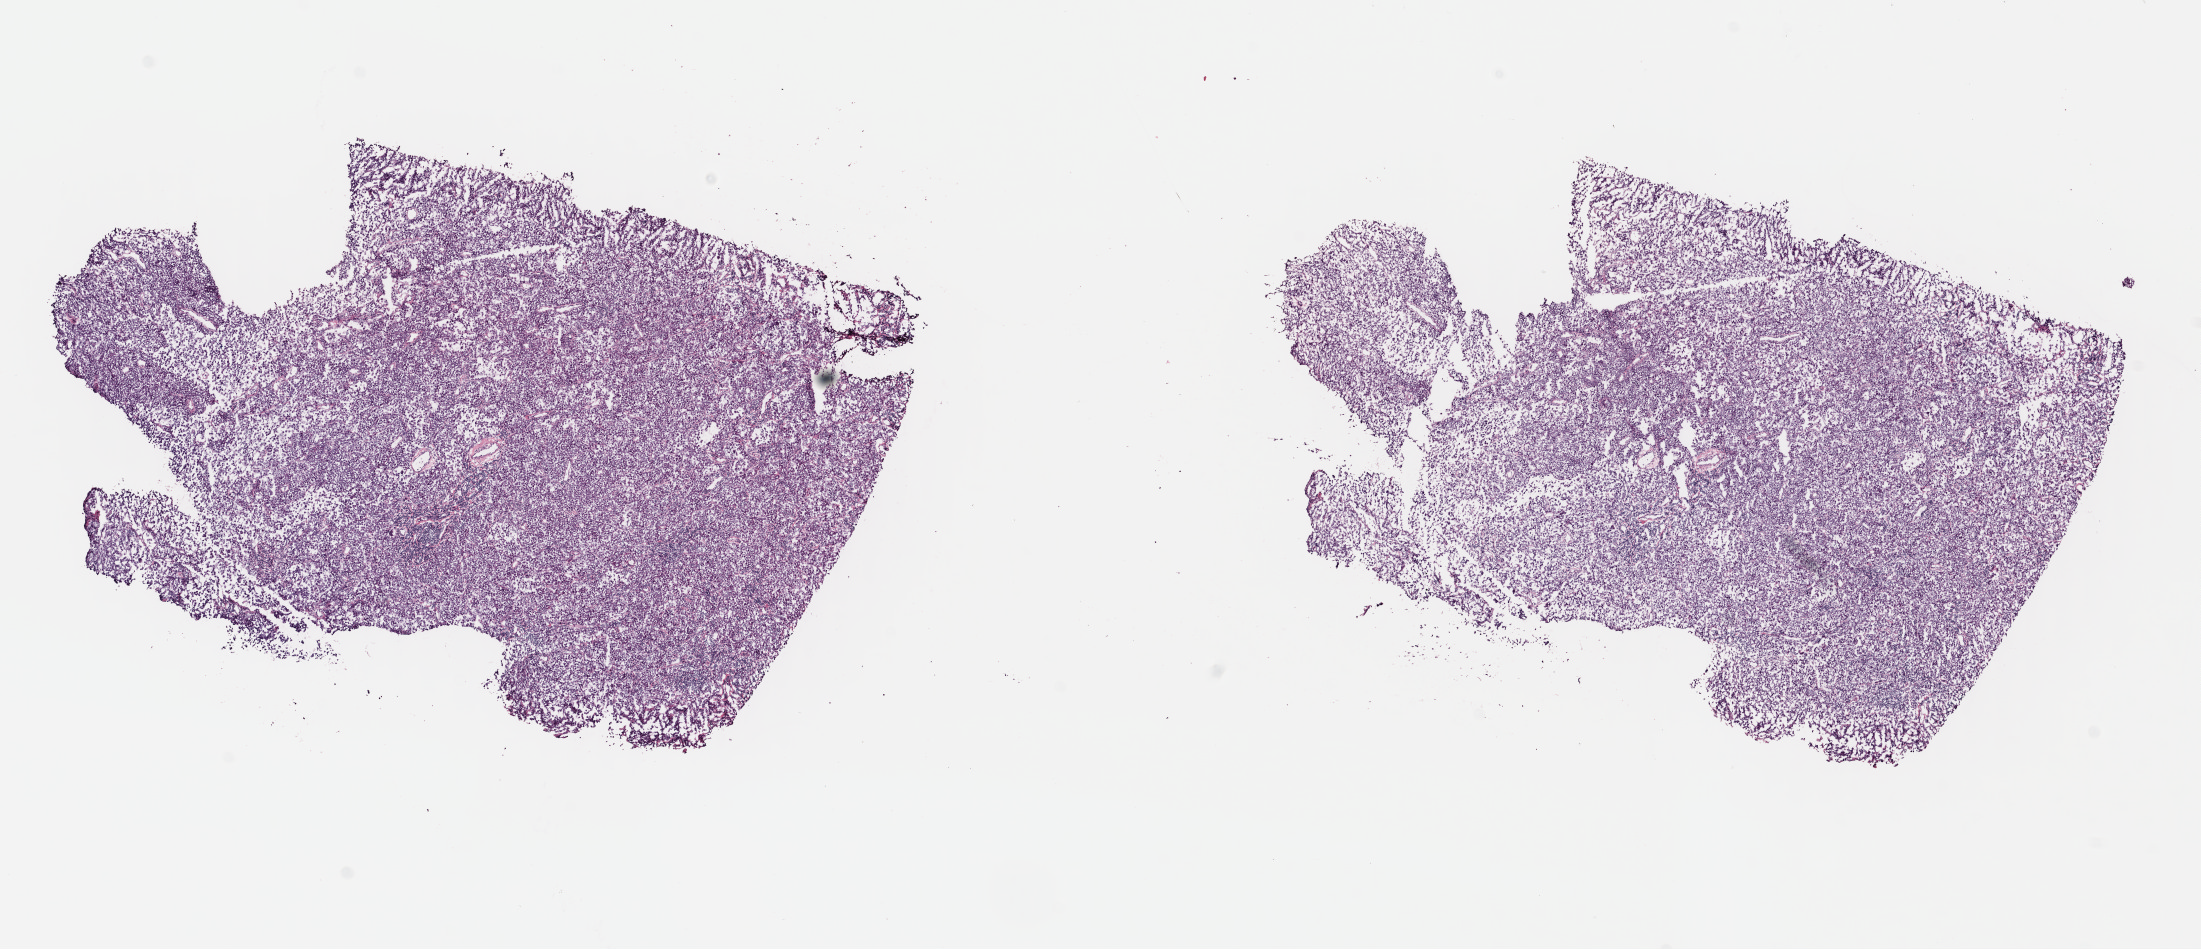
Digitized H&E tissue section (whole slide) — whole scanned area (about 17.3 x 7.5 mm, acquisition: 40x scan) shown as a low-resolution overview, frozen section, metastatic tumour sample. Patient: male, age at initial diagnosis 35 years. Slide review estimates, as recorded: tumour cells 80%, tumour nuclei 80%, normal cells 0%, stromal cells 20%, necrosis 0%. Infiltration values recorded for this section: lymphocyte infiltration 3%, monocyte infiltration 1%, neutrophil infiltration 0%.
• this section: metastatic tumour tissue
• patient diagnosis: Malignant melanoma, NOS